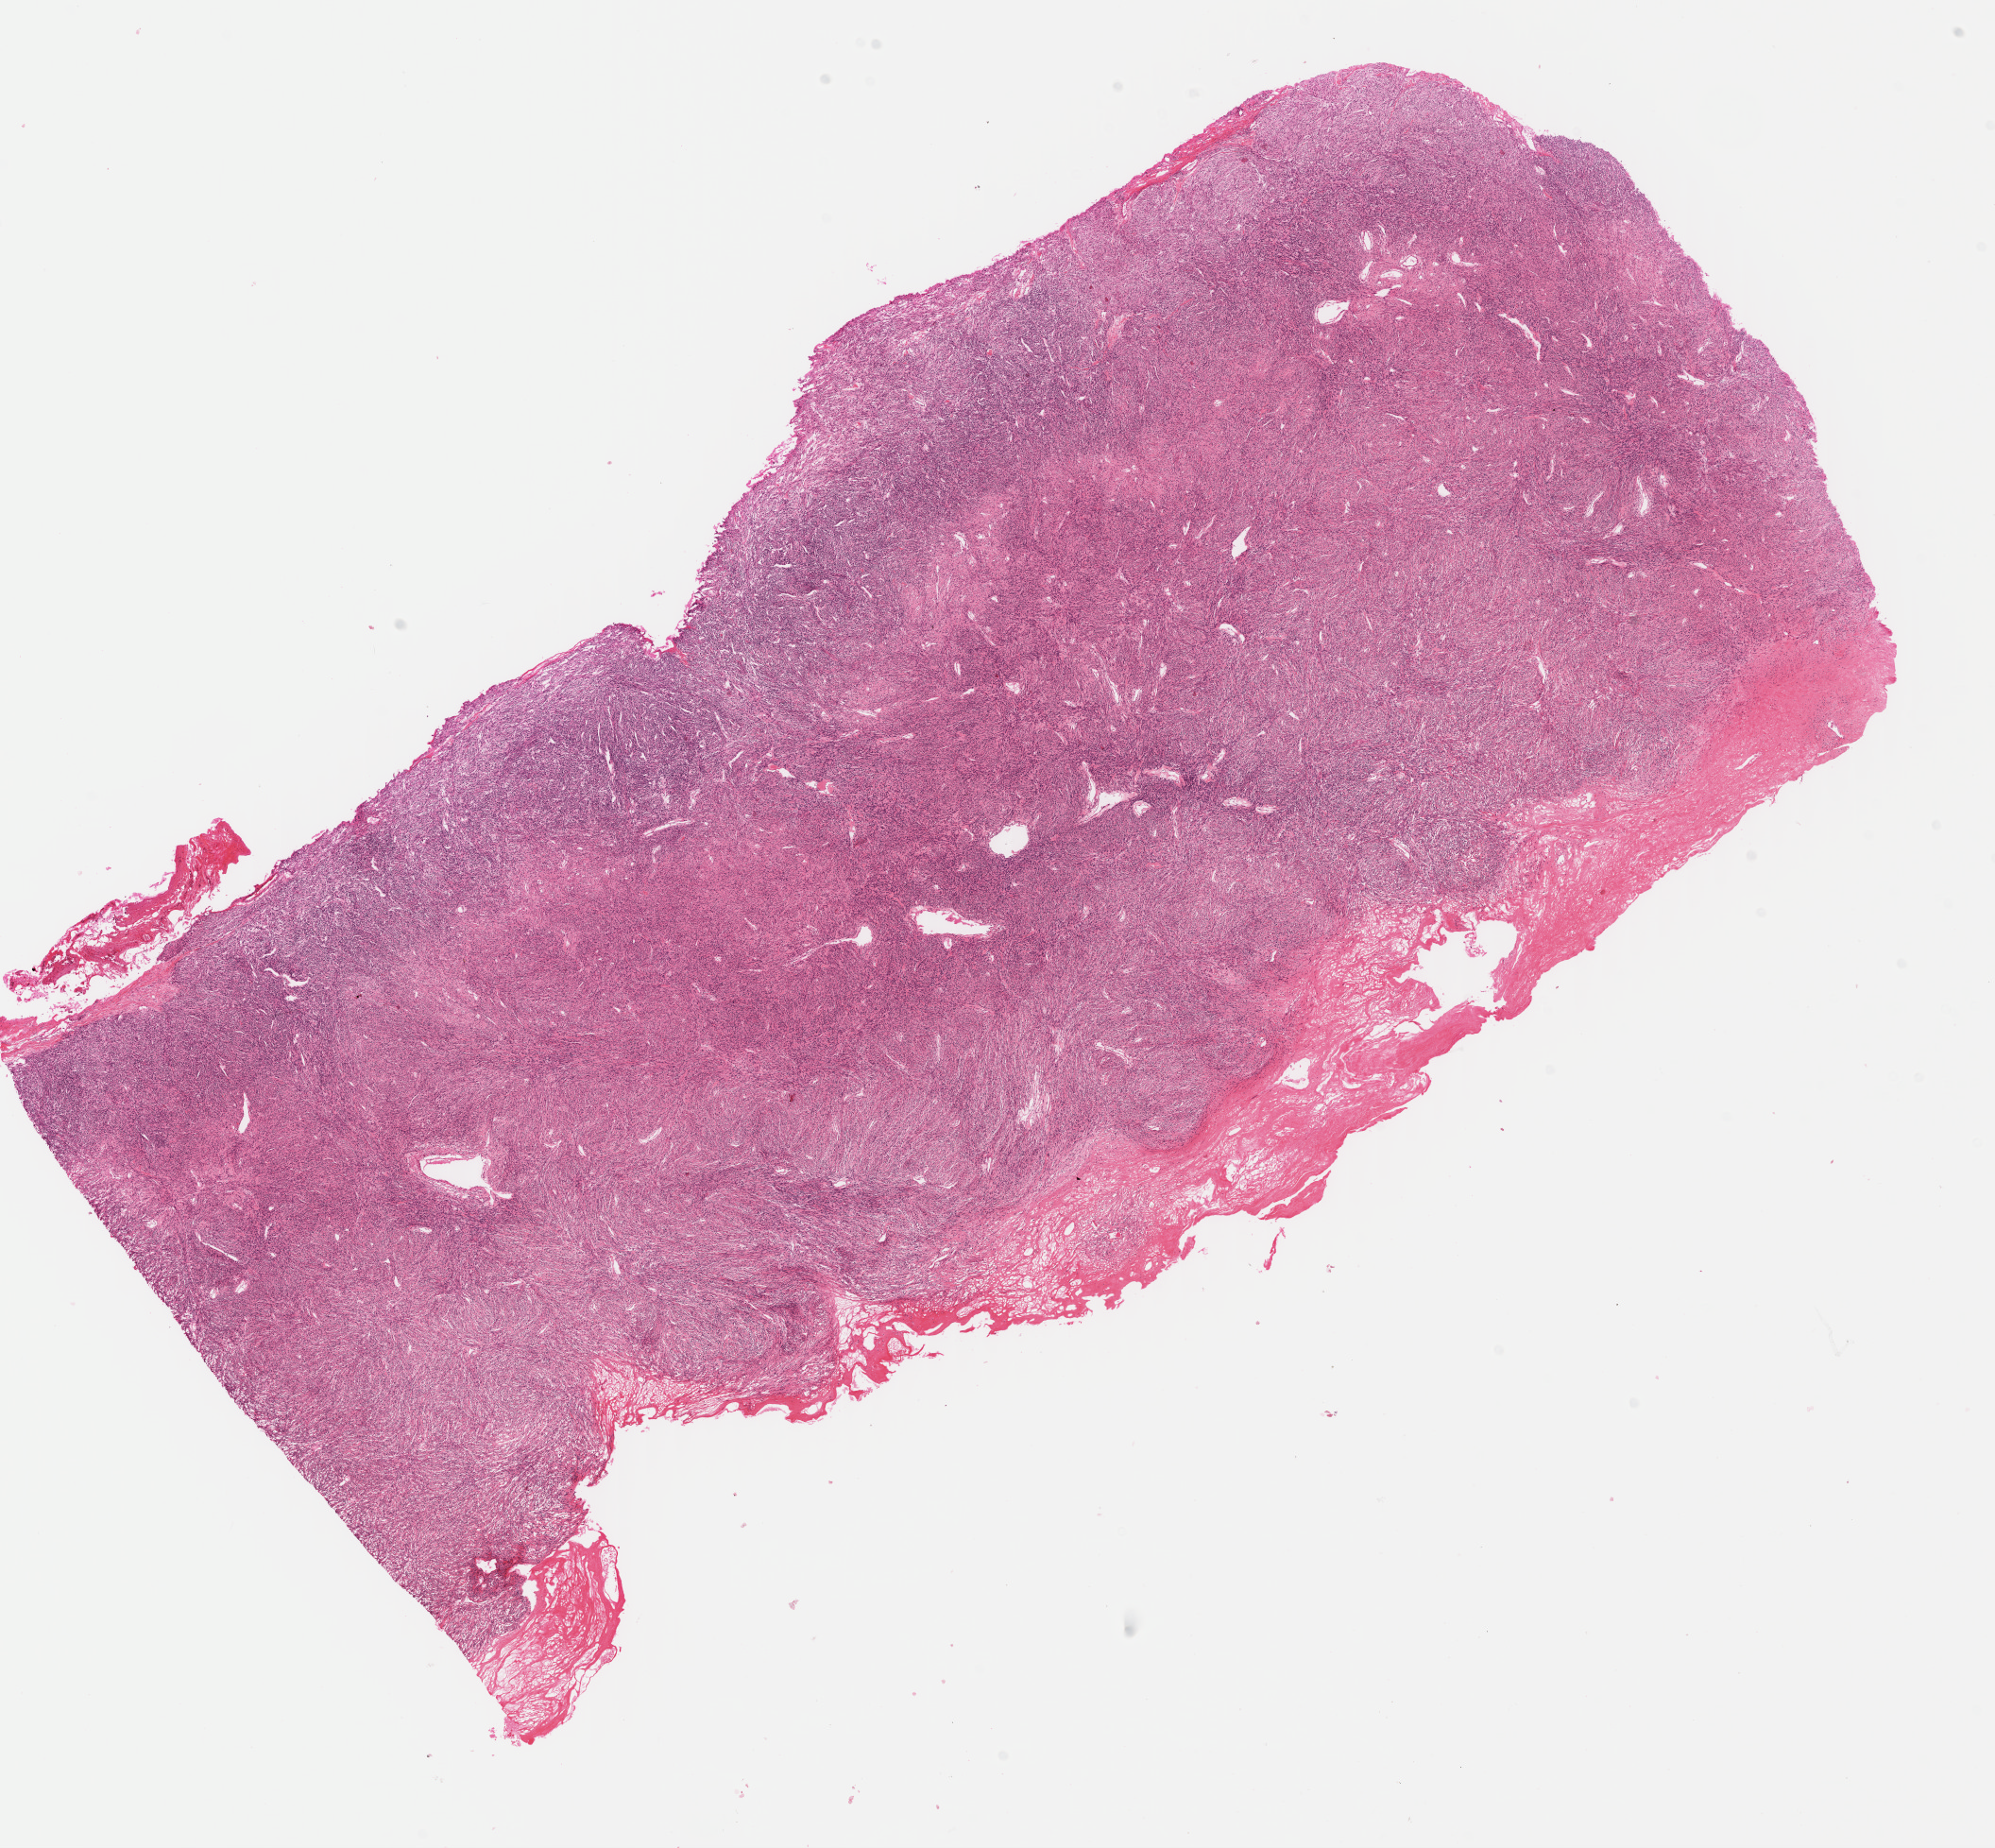
Hematoxylin and eosin (H&E) stained whole-slide image — low-resolution overview of the scanned area, about 16.6 x 15.4 mm; FFPE section; retroperitoneum and peritoneum, primary tumour sample. Patient: female, age at initial diagnosis 77 years.
Histologic diagnosis: Leiomyosarcoma, NOS (retroperitoneum).